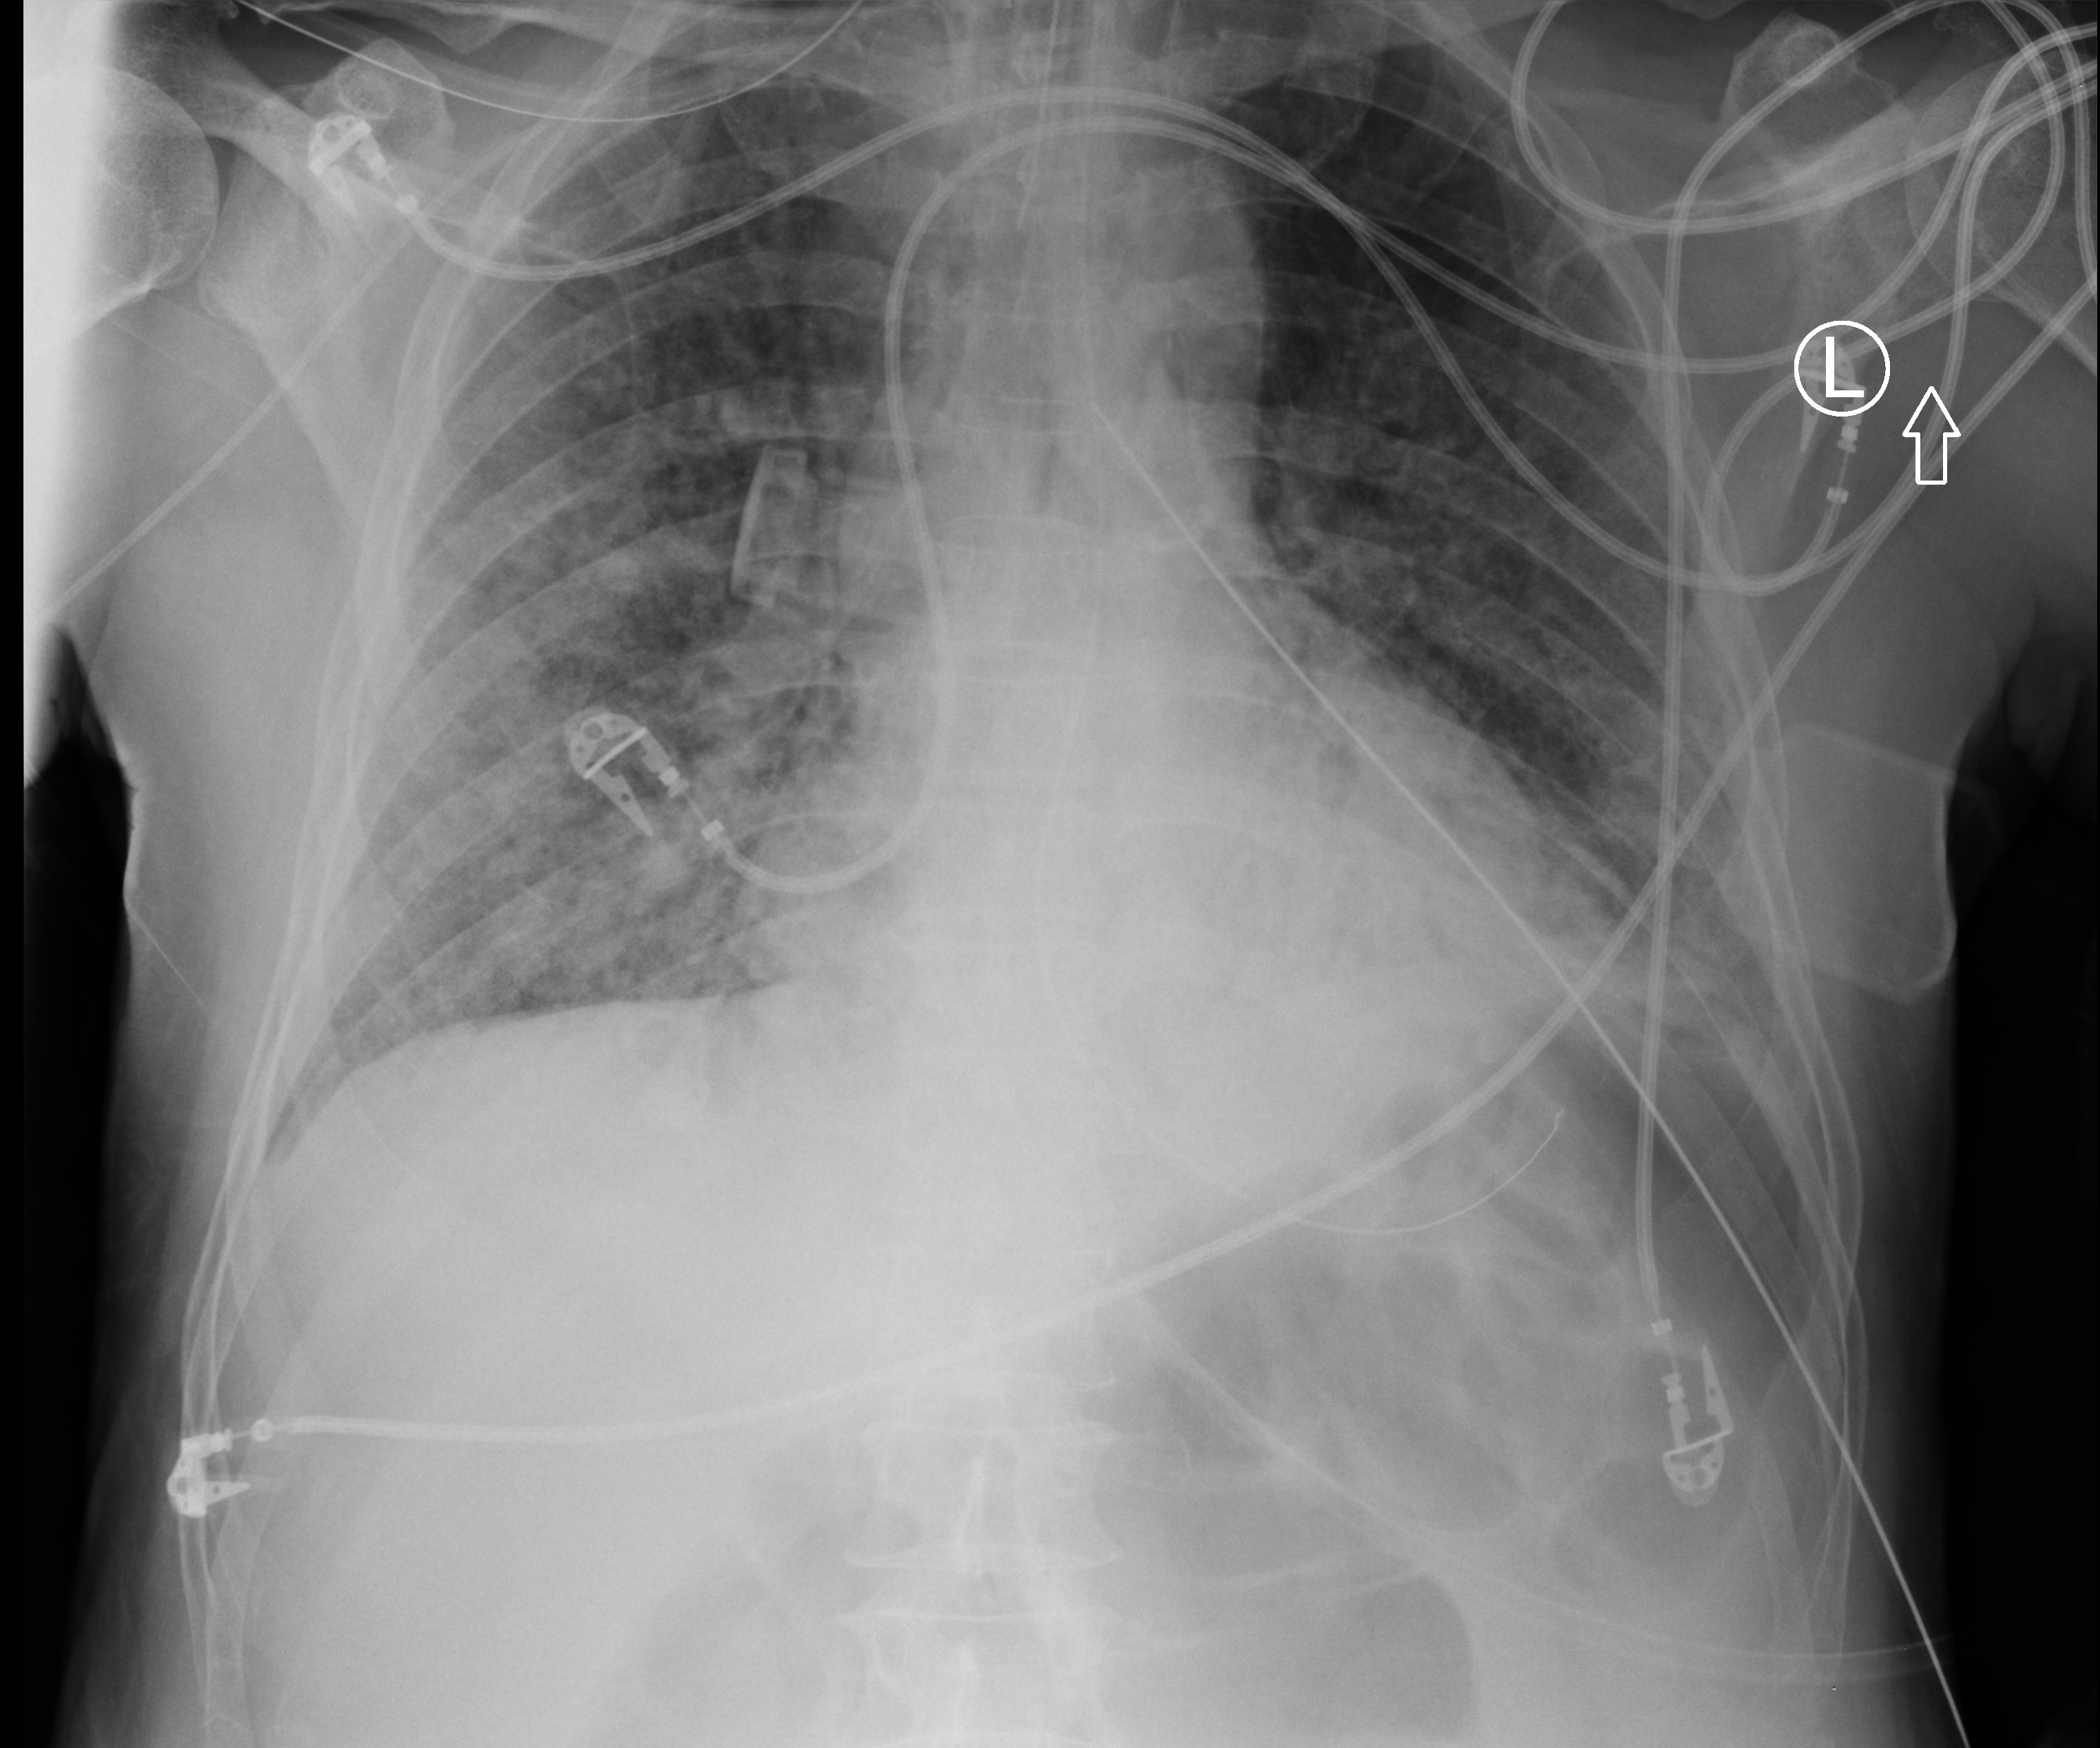
Bedside chest radiograph (computed radiography). Patient hospitalised with COVID-19; male, aged 60–74 years.
From the hospital-stay record, not from the radiograph (when in the stay this image was taken is not recorded):
- other chronic lung disease (admission record): no
- mechanically ventilated during this hospital stay: yes
- hypertension (admission record): yes